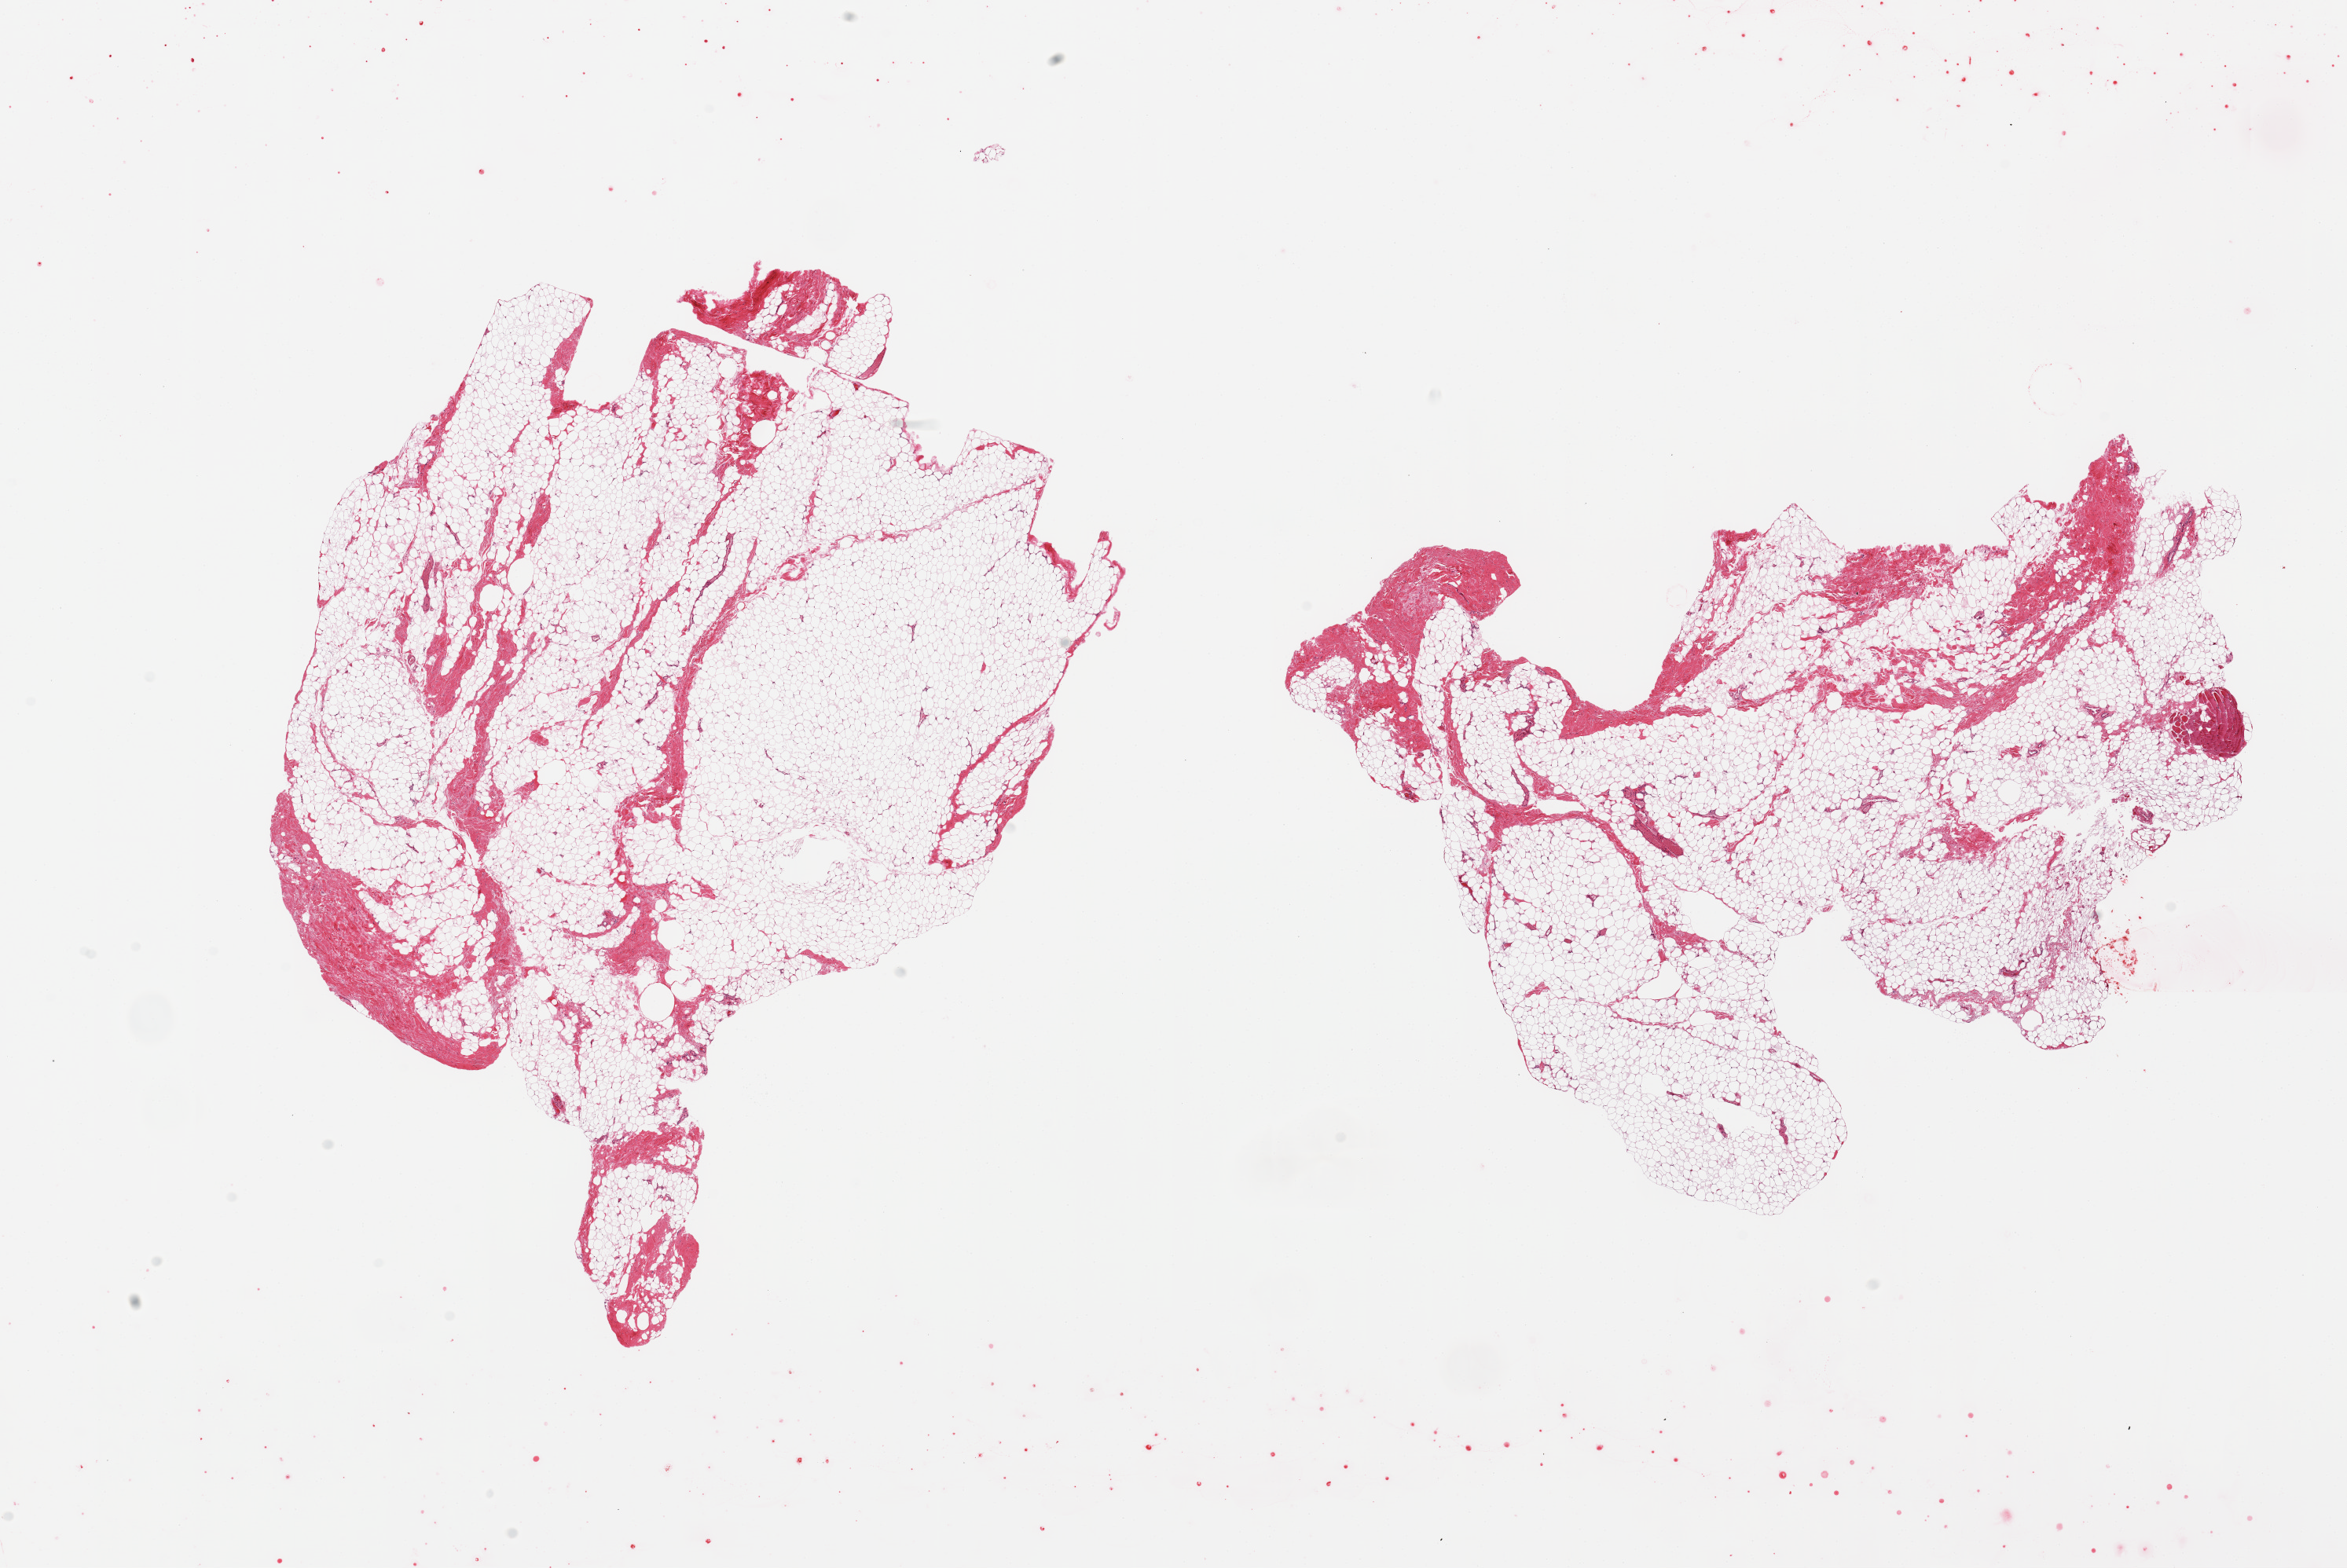
Whole-slide image, hematoxylin and eosin (H&E) stain, shown as a low-resolution overview of the whole scanned area (about 23.6 x 15.8 mm, slide scanned at 20x). PAXgene-fixed, paraffin-embedded tissue. Section of breast (target tissue). Donor tissue sample.
Pathologist's review note for this sample: 2 pieces, fibroadipose elements only no ducts.